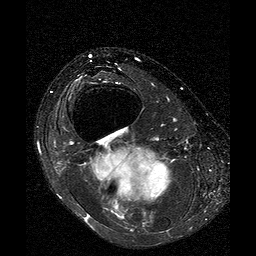
MRI of an extremity soft-tissue mass, one axial slice; position 23 of 25 along the scan axis; T2-weighted fat-saturated; 256 × 256 image matrix, field of view 160 × 160 mm. Female patient. Case-level facts recorded for this patient, not image findings: histological type: liposarcoma; site of the primary tumour: right thigh.
Structures marked on this image (outlined manually by an expert reader):
- gross tumour volume (mass): bounding box <88,145,171,205> (left, top, right, bottom; pixels)